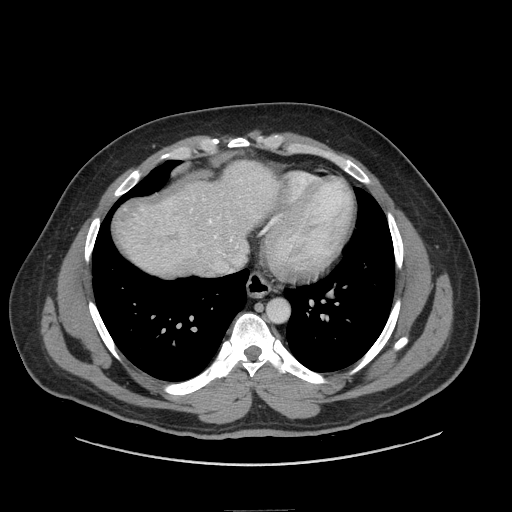
Contrast-enhanced abdominal CT (liver protocol), one axial slice. Slice 74 of 87 in the series (ordered by position). Reconstruction kernel STANDARD. Soft-tissue window (W 400 / L 40 HU). 512 × 512 image matrix, field of view 440 × 440 mm. From the clinical record (not read from this slice): diagnosis: hepatocellular carcinoma (patient treated with transarterial chemoembolisation; whether this scan precedes or follows treatment is not stated here); TNM stage (as recorded): Stage-II; Child-Pugh class: A; tumour differentiation: moderately differentiated.
Structures marked on this image (semi-automatic segmentation, software-assisted and operator-edited):
- abdominal aorta: box from (x=268, y=301) to (x=288, y=321) px
- liver parenchyma outside the tumour (the mass and vessels are separate outlines, so this box may not span the whole liver): (x=114, y=162)–(x=272, y=274)
- liver vessels: (x=209, y=220)–(x=217, y=238)